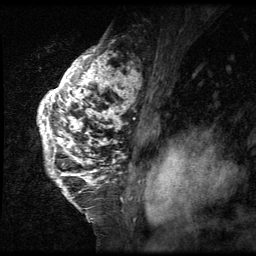
Breast MRI (dynamic contrast-enhanced), one sagittal slice; slice 44 of 64 in the series (ordered by position); 3 images stored at this slice position (order not interpretable as contrast timing); 1.5 T; TE 4.2 ms, TR 9 ms; 2.5 mm slice thickness; 256 × 256 image matrix, field of view 180 × 180 mm. Female patient, age 50 years. From the clinical record (not read from this slice): setting: breast cancer imaged before/during neoadjuvant chemotherapy; receptor status: triple-negative.
Structures marked on this image (semi-automatic segmentation, software-assisted and operator-edited):
- analysis volume of interest (the breast-tissue region the enhancement analysis was run in; not a lesion): bounding box [x1, y1, x2, y2] px = [37, 39, 139, 212]
- tumour enhancement mask (voxels above the 140 % enhancement threshold inside the analysis volume of interest): [37, 46, 139, 200]